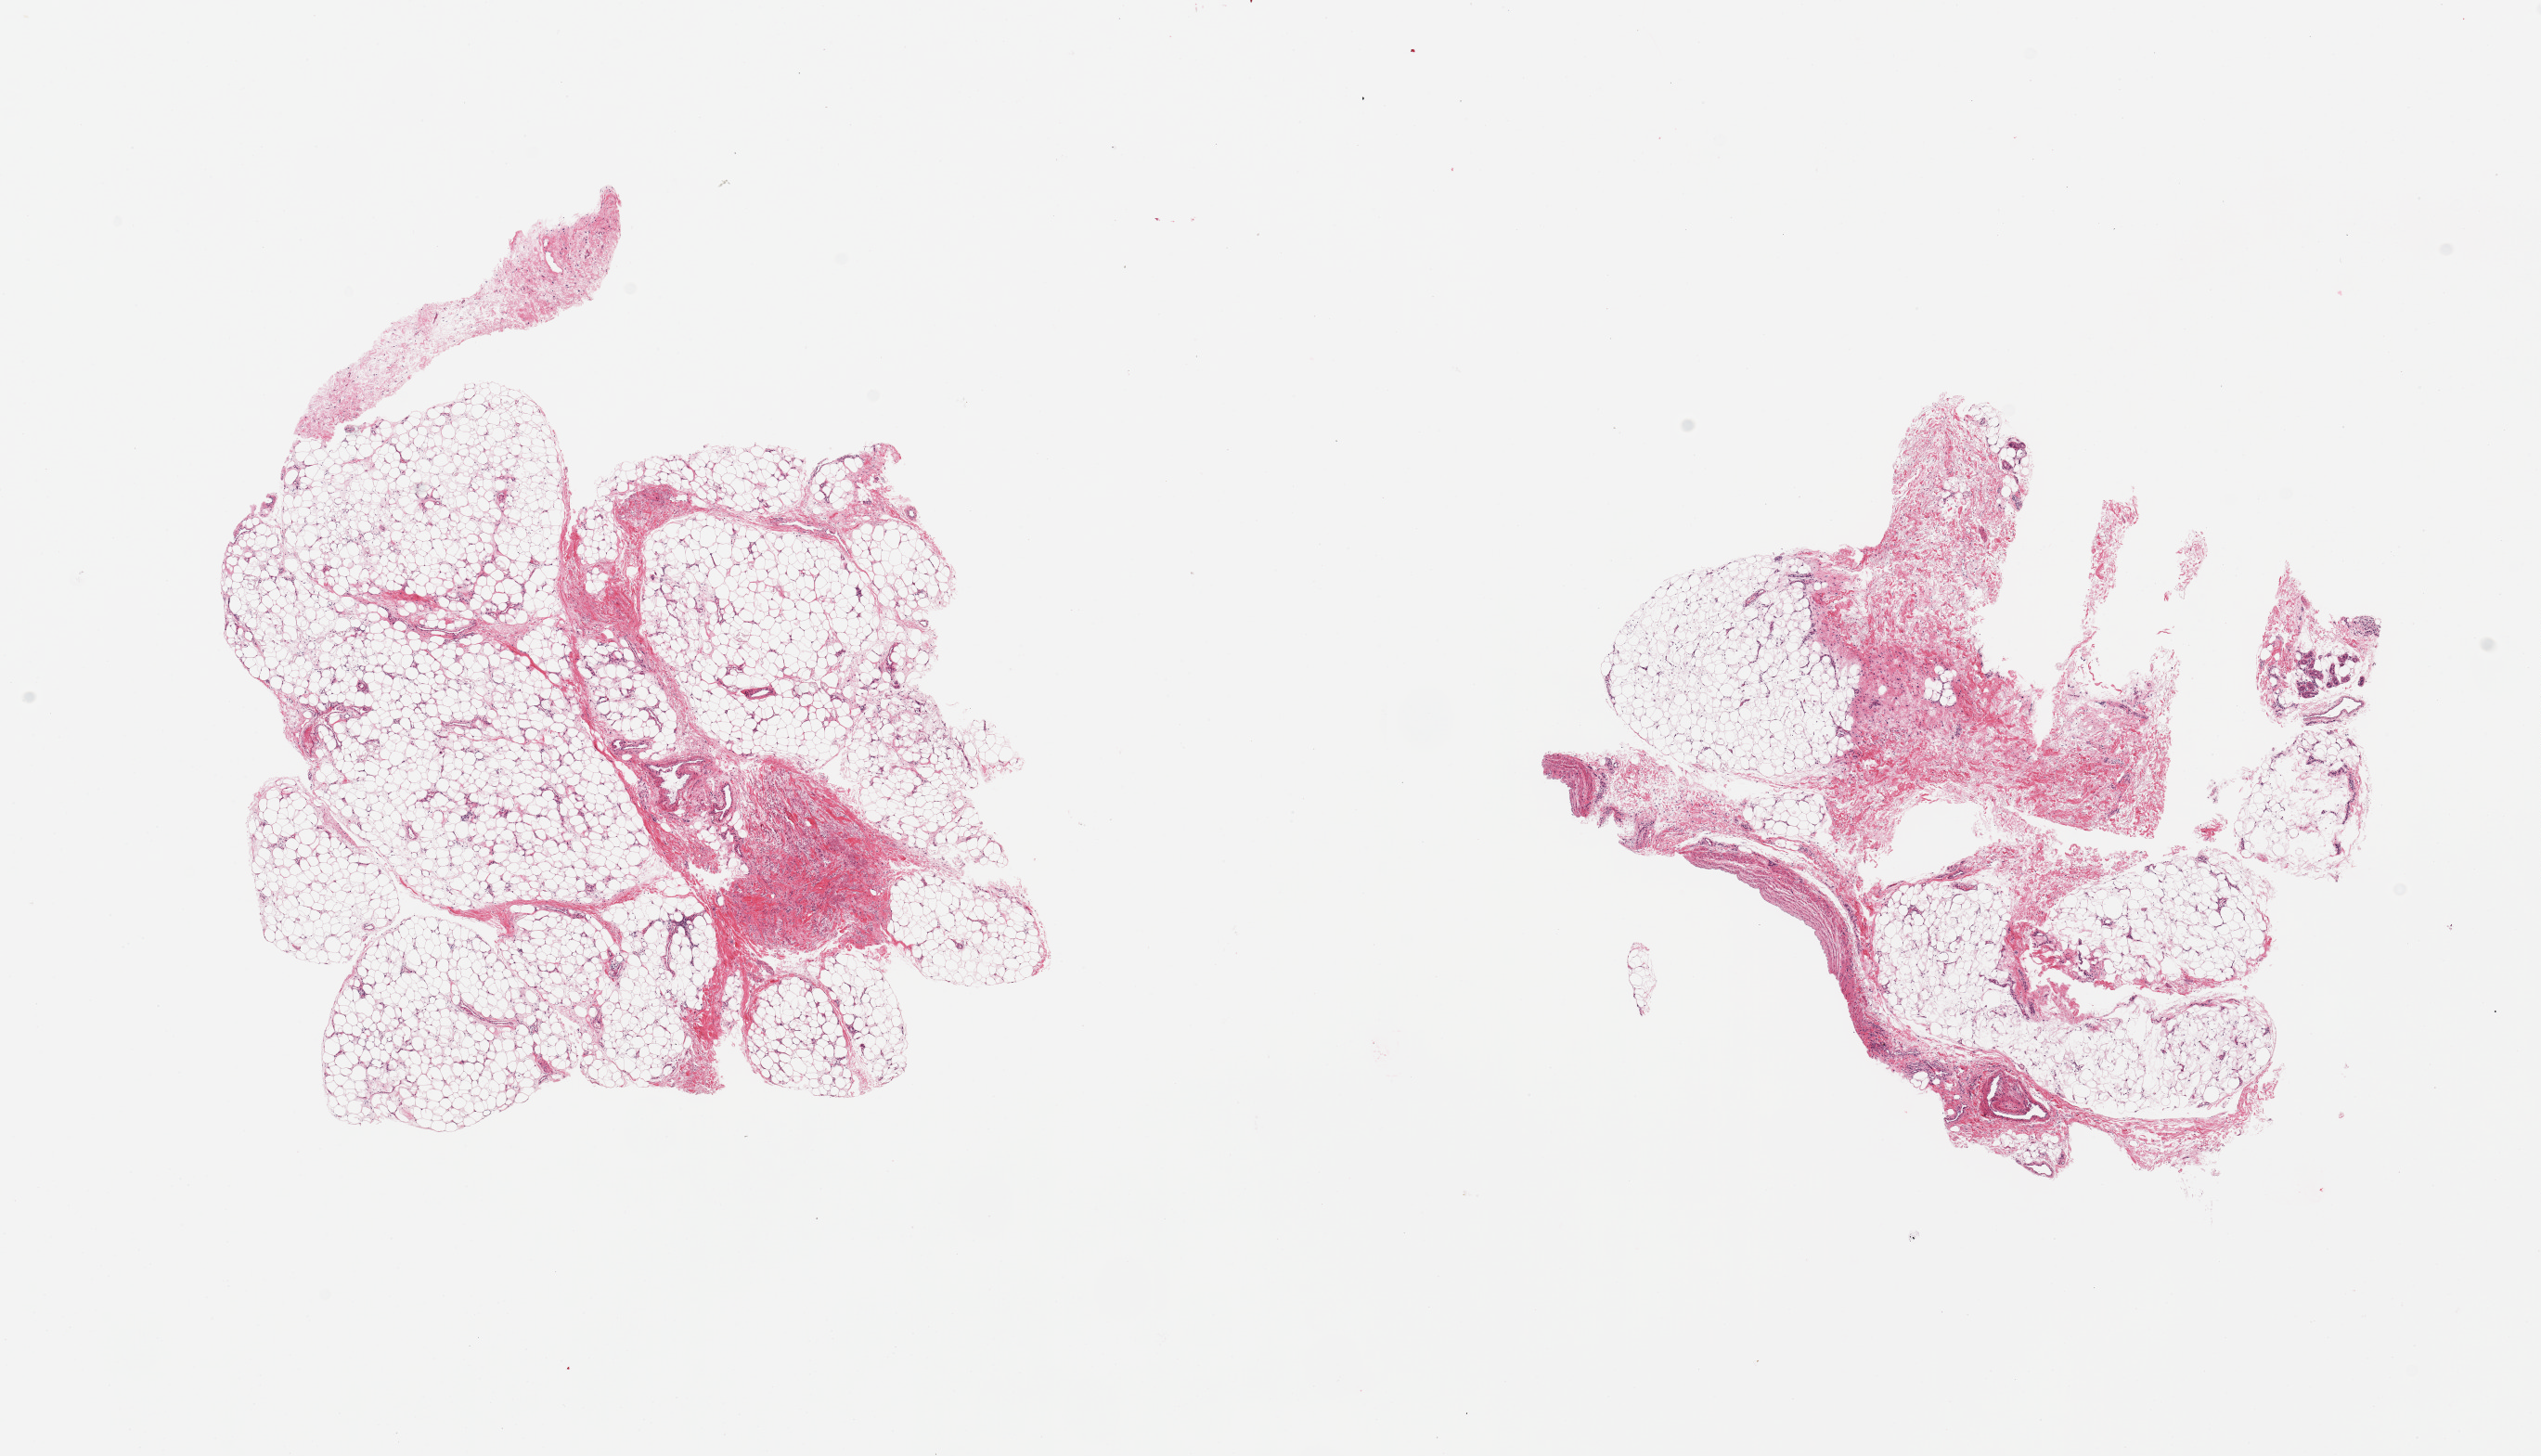
Whole-slide image, hematoxylin and eosin (H&E) stain — whole scanned area (about 21.7 x 12.4 mm, from a 20x scan) shown as a low-resolution overview; PAXgene-fixed paraffin-embedded (PFPE) section; target tissue: adipose tissue; donor tissue sample. Donor: male.
Pathologist's review note for this sample: 2 pieces; 20% of one and 50% of second is fibrous and vascular tissue with some sweat glands.